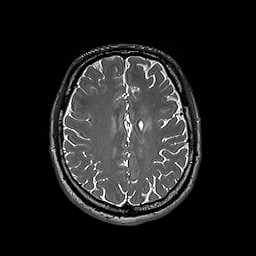
Brain MRI from a brain-tumour surgery series, one axial slice. 256 × 256 image matrix, field of view 250 × 250 mm. Case-level facts recorded for this patient, not image findings: histopathology: Oligodendroglioma; WHO grade: 3; IDH mutation: yes; tumour location: Left Frontal.
Outlined on this slice (outlined manually by an expert reader):
- tumour: box from (x=143, y=118) to (x=153, y=130) px